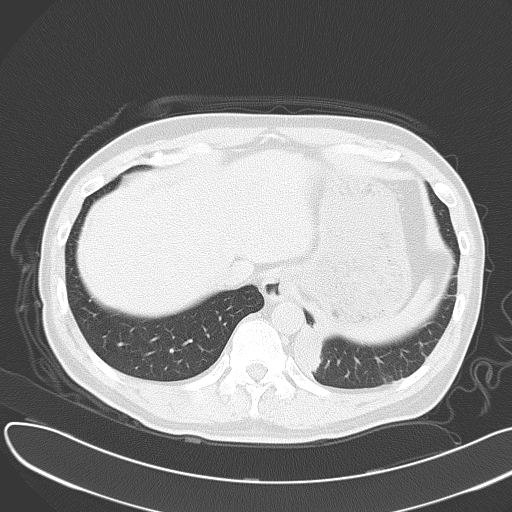
Chest CT, one axial slice. Position 8 of 55 along the scan axis. Reconstruction kernel B70f. 120 kVp. Lung window (W 1500 / L -600 HU). 5 mm slice thickness. 512 × 512 image matrix, field of view 376 × 376 mm. Patient: male, 55 years. Case-level facts recorded for this patient, not image findings: clinical TNM (as recorded): T2 N3 M0; histopathological grade: G3.
Annotated regions visible in this slice (rectangle marked by the reading radiologist):
- lung tumour (recorded histology: small cell carcinoma): bounding box <289,323,331,376> (left, top, right, bottom; pixels)